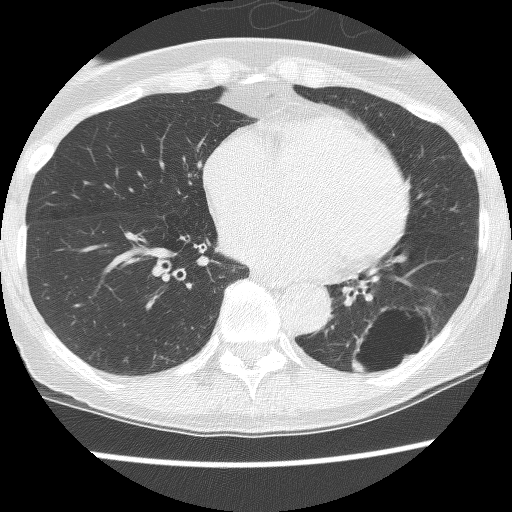
Low-dose screening chest CT, axial slice. Third annual screen. Lung window (W 1500 / L -600 HU). 2.5 mm slice thickness. Lung (sharp) reconstruction kernel (BONE). 512 × 512 image matrix. Female, age 61 years at enrolment. Current smoker at enrolment.
- Expert reader's lesion annotation, bounding box (x1, y1, x2, y2) in pixels: (329, 289, 449, 390).
- The screening reader recorded 2 non-calcified nodules or masses ≥4 mm on this exam; which of them this box marks is not recorded.